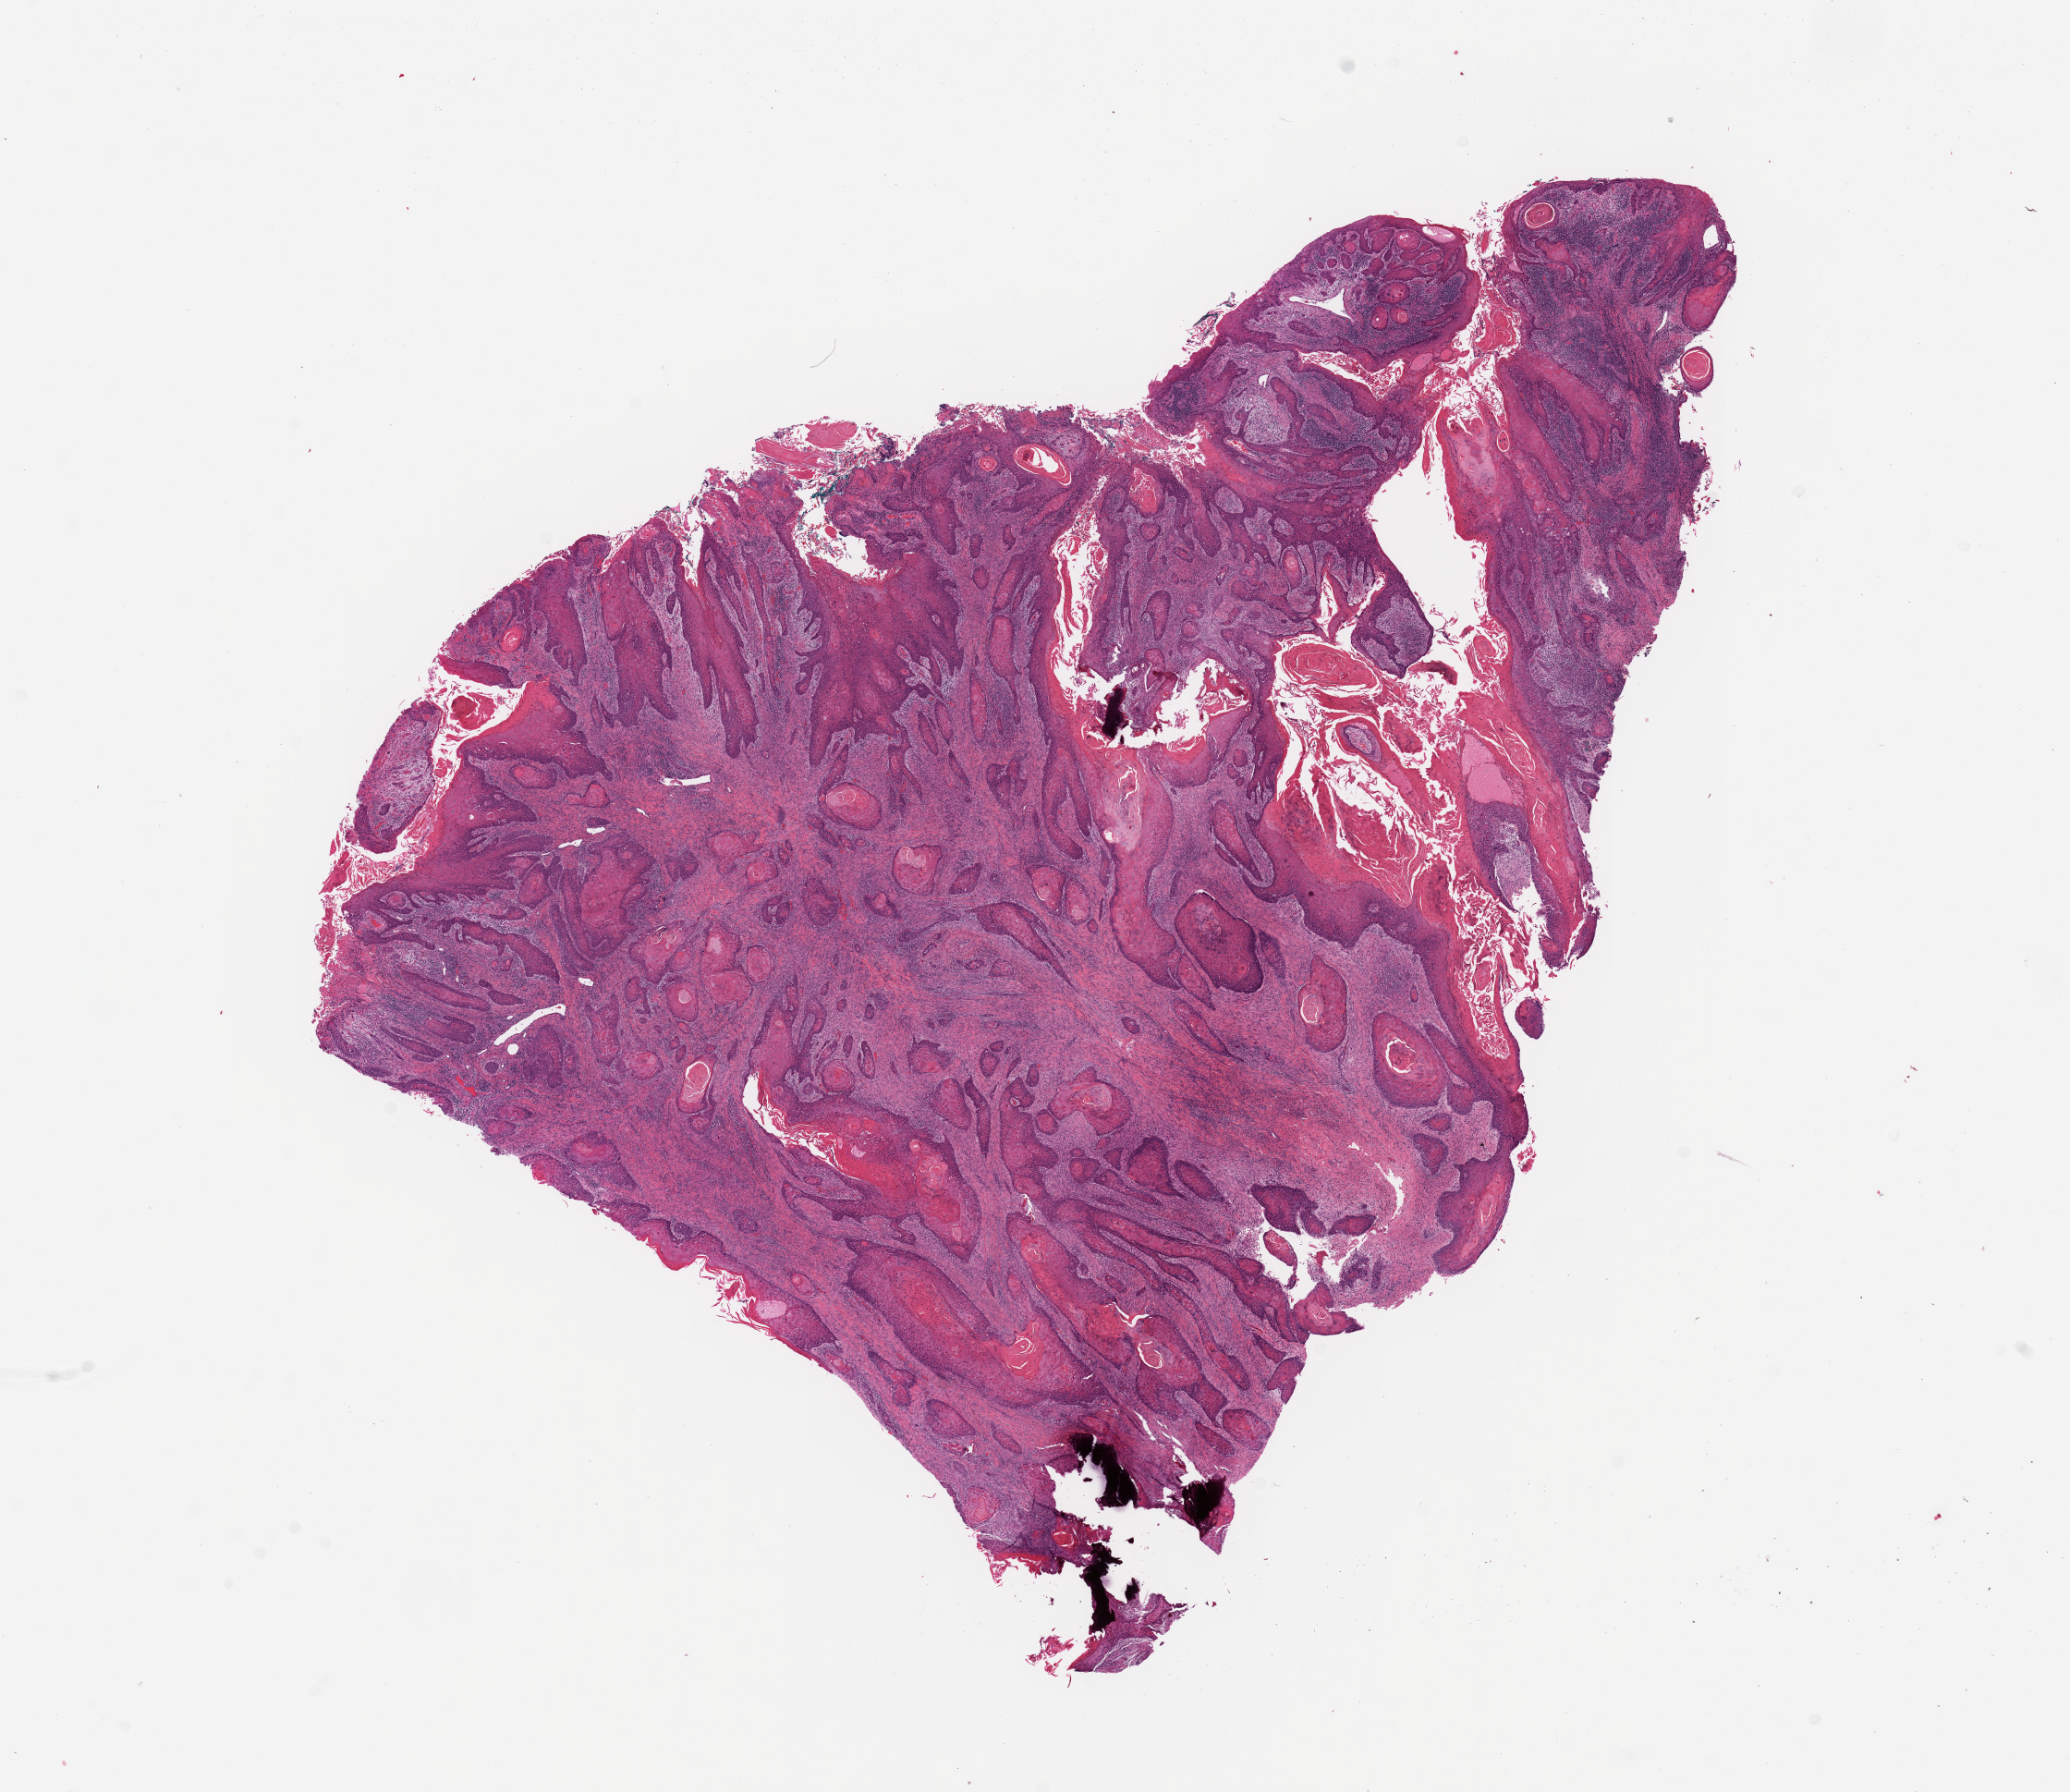
Hematoxylin and eosin (H&E) stained whole-slide image, whole scanned area (about 17.7 x 15.3 mm, slide scanned at 20x) shown as a low-resolution overview, head and neck, tissue type not recorded. Male, 56 y/o.
Patient diagnosis: Squamous cell carcinoma, NOS (cheek mucosa).